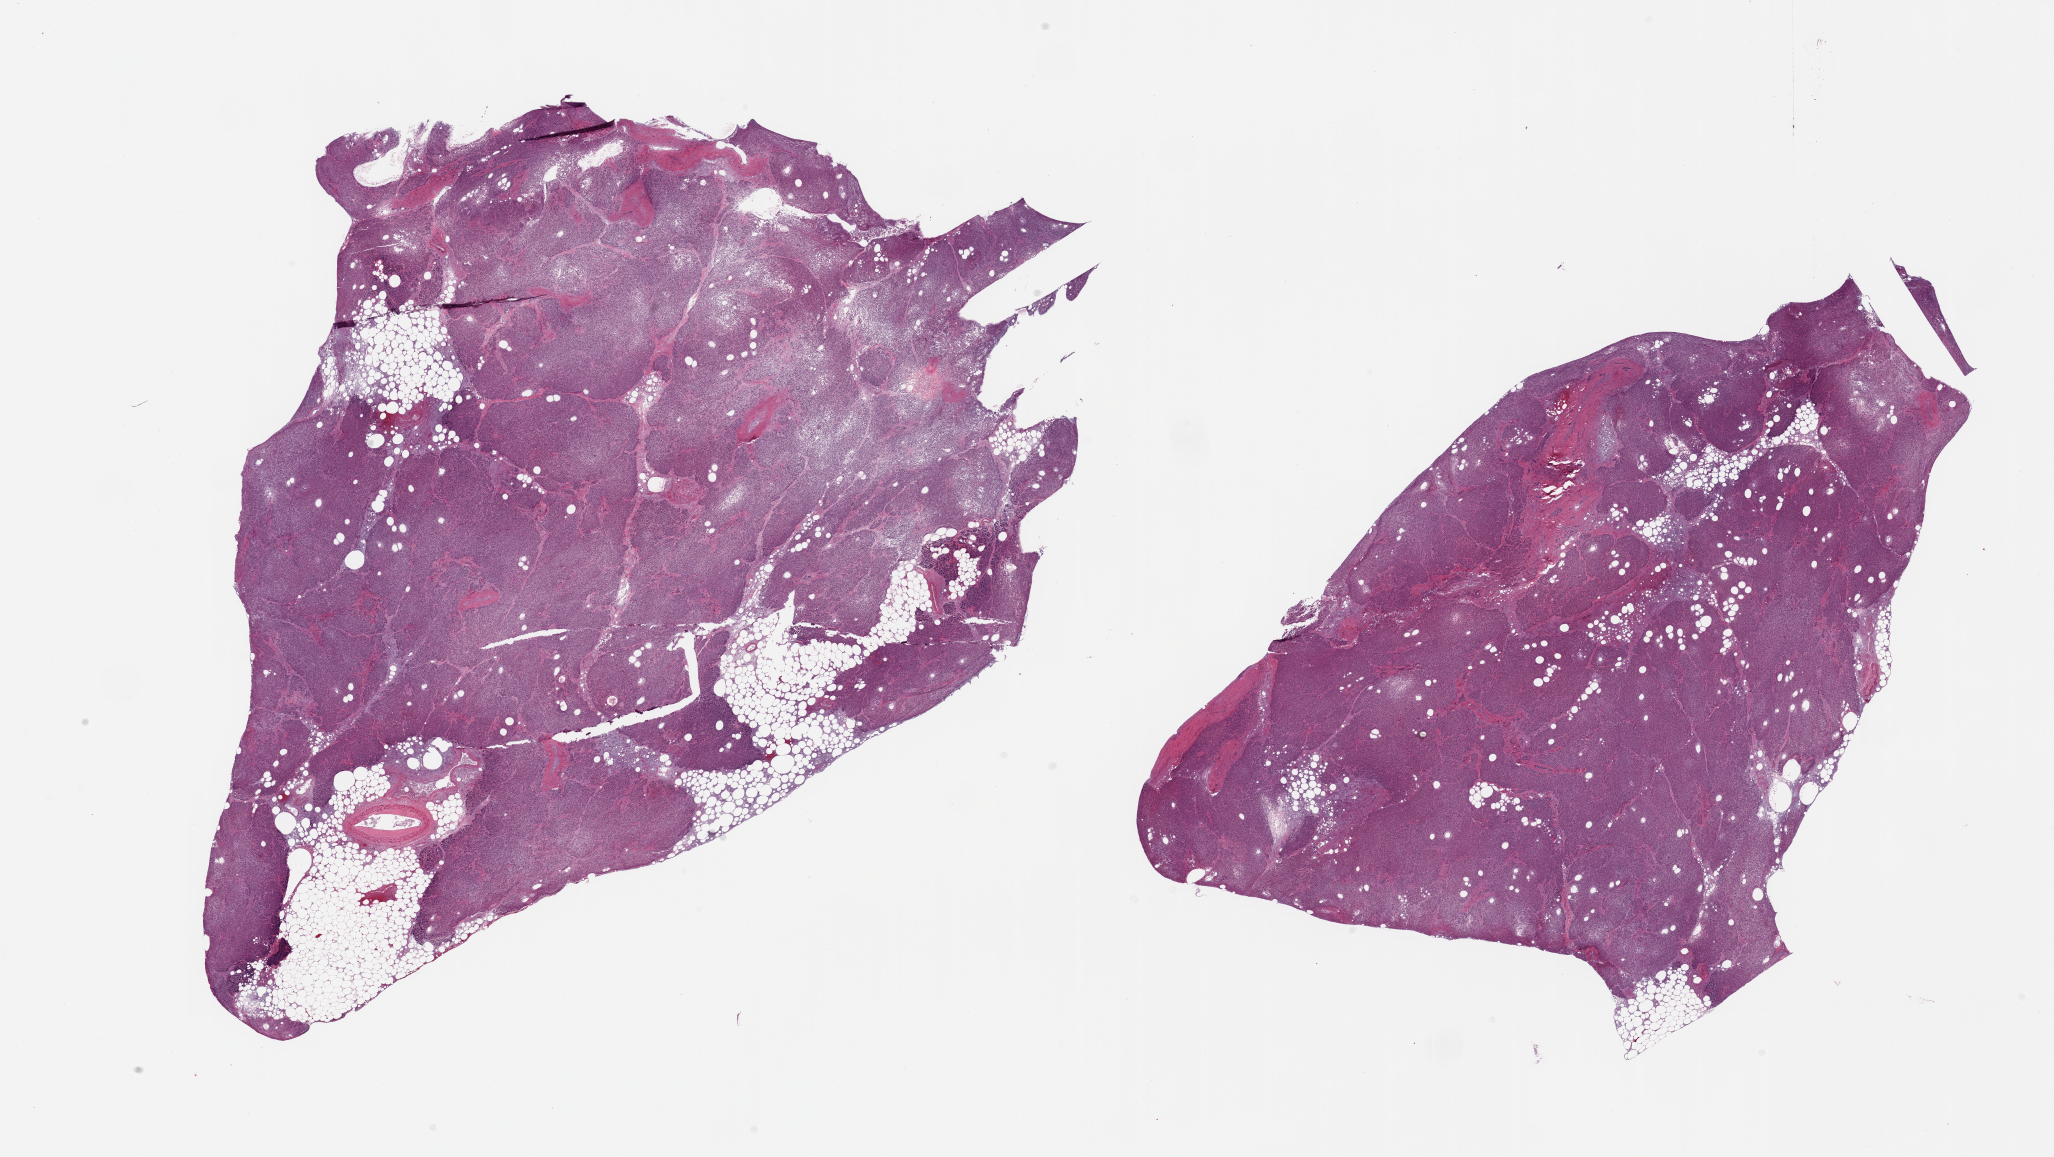
Whole-slide image, hematoxylin and eosin (H&E) stain, brightfield — whole scanned area (about 32.5 x 18.3 mm) shown as a low-resolution overview, PAXgene-fixed, paraffin-embedded tissue, target tissue: pancreas, donor tissue sample. Male donor.
Pathologist's review note for this sample: 2 pieces; extensive autolysis.